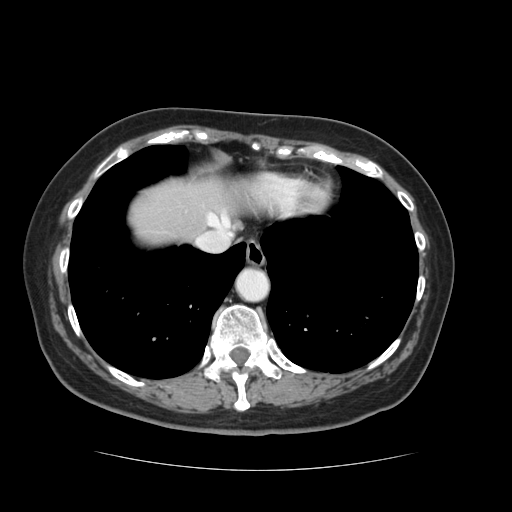
Contrast-enhanced abdominal CT, one axial slice. Slice 114 of 128 in the series (ordered by position). Intravenous contrast given. Soft-tissue window (W 400 / L 40 HU). 2.5 mm slice thickness. 512 × 512 image matrix. Female patient, age 67 years. From the clinical record (not read from this slice): diagnosis: colorectal cancer liver metastases, imaged before liver resection.
Structures marked on this image (expert manual segmentation):
- hepatic veins: bounding box (x1, y1, x2, y2) in pixels: (197, 213, 233, 250)
- liver: (131, 179, 231, 245)
- planned liver remnant (the part of the liver to remain after resection): (131, 186, 232, 245)